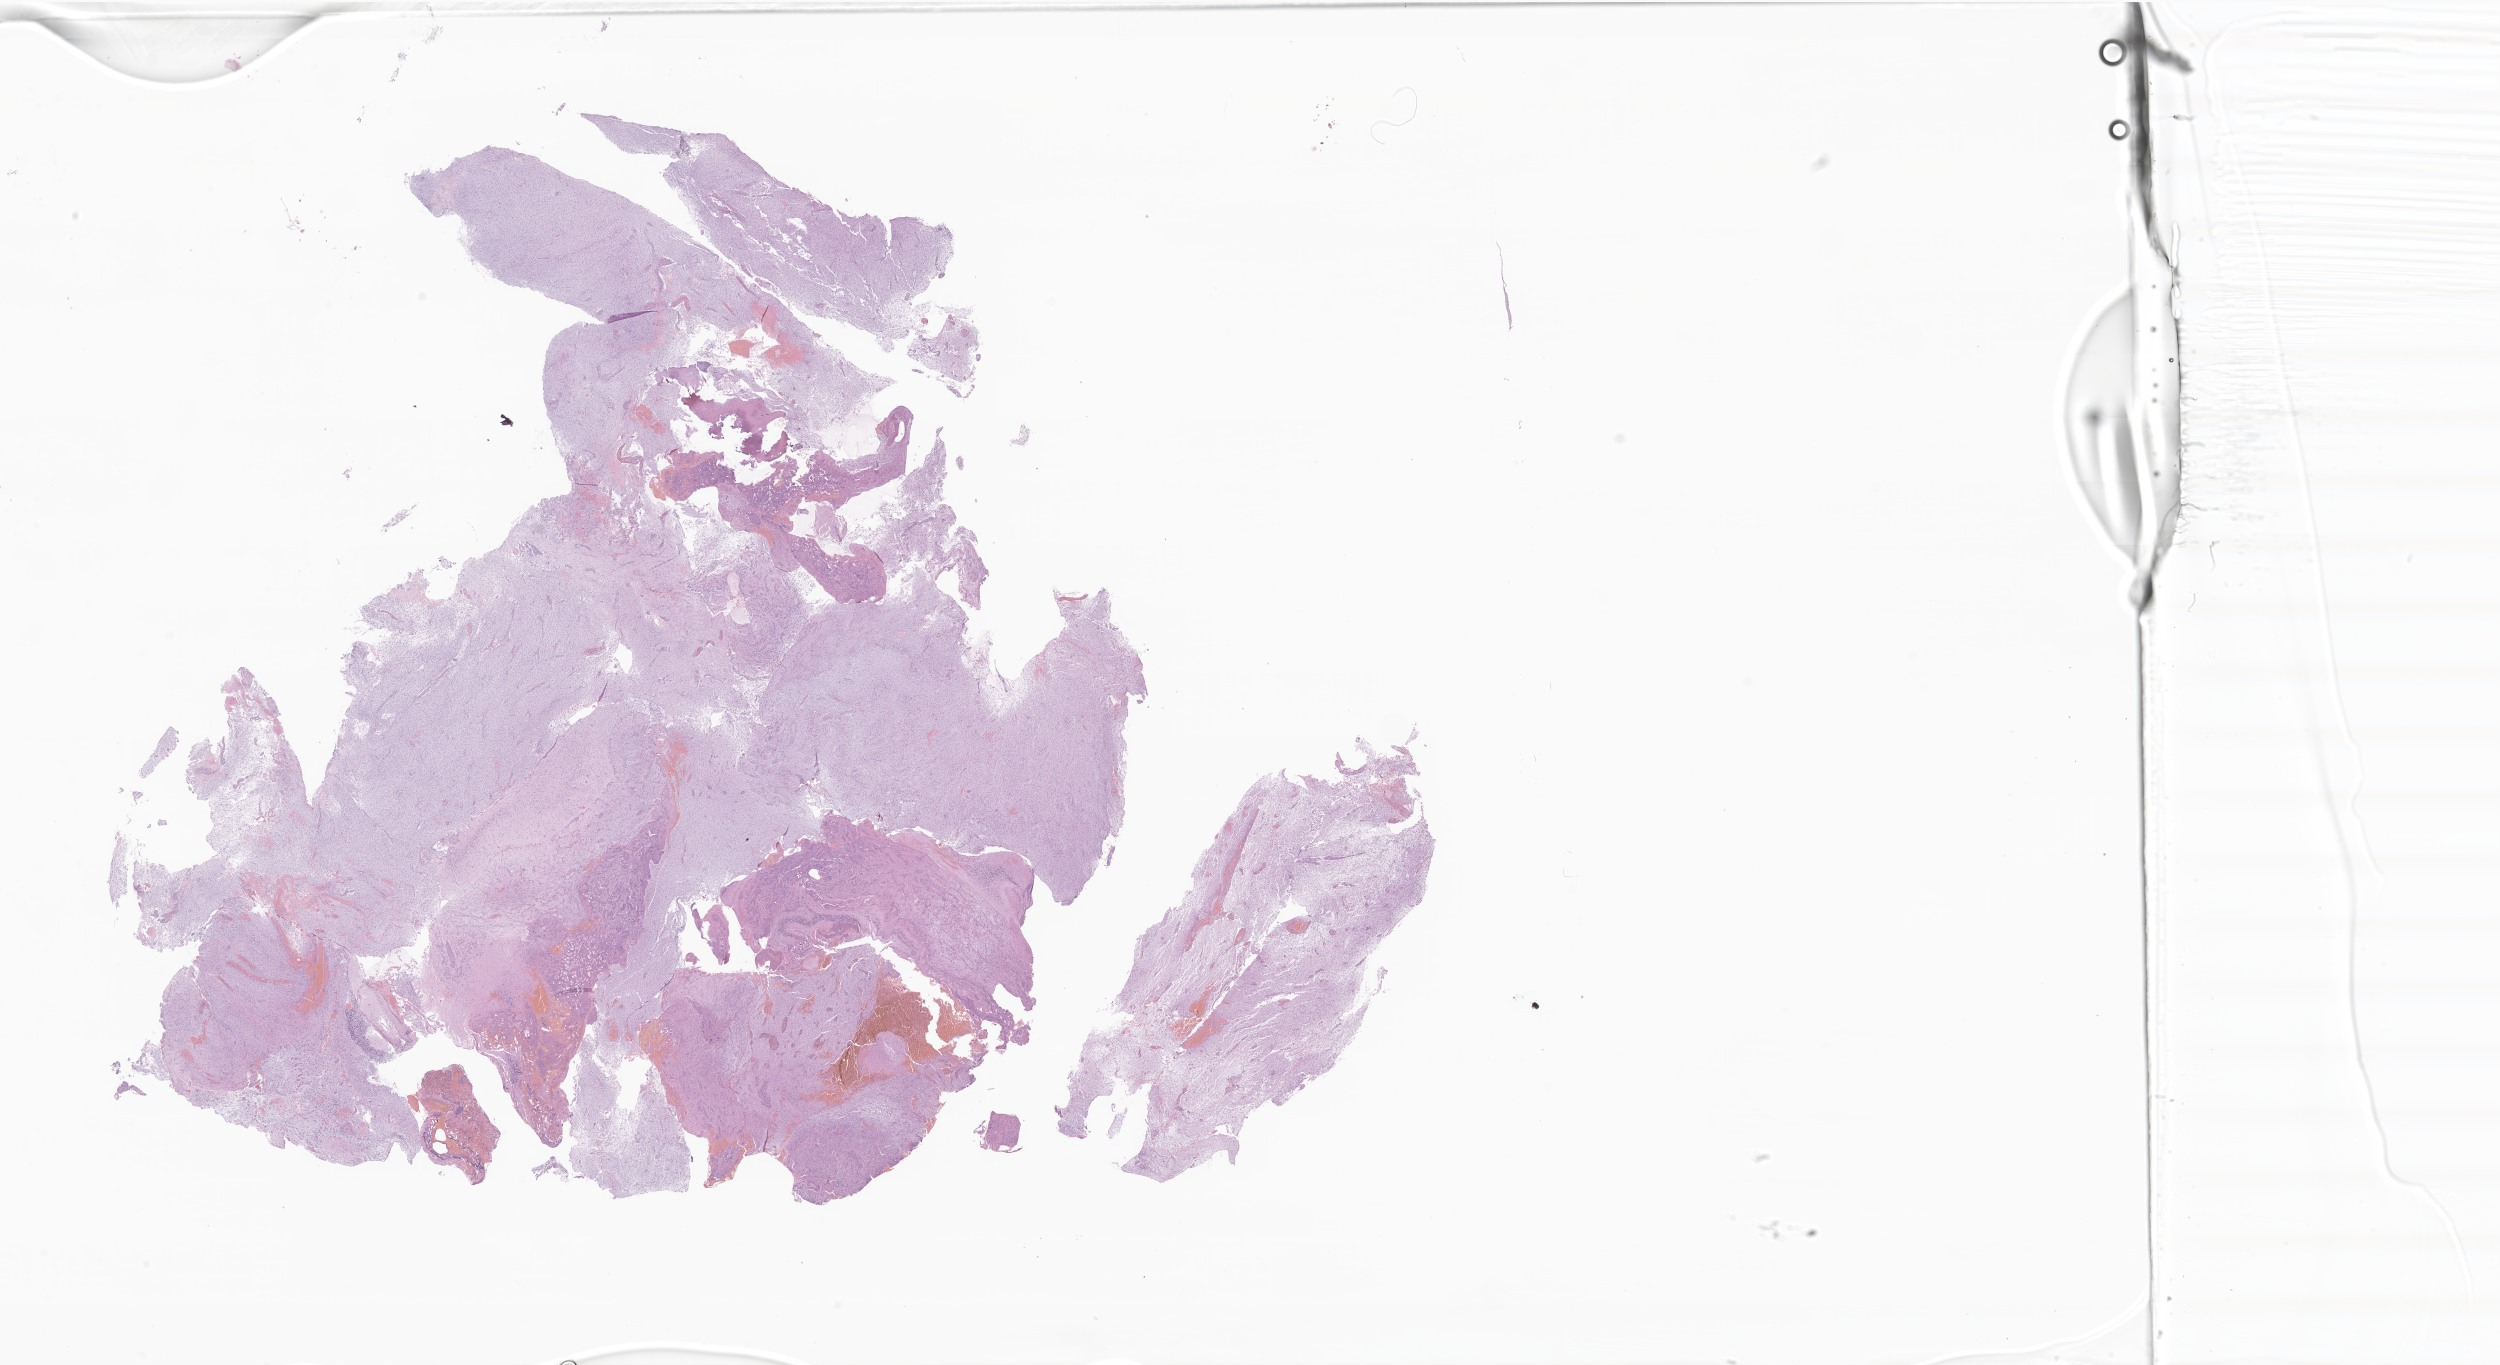
H&E whole-slide image of tumor tissue from the brain, whole scanned area (about 42.2 x 23.0 mm) shown as a low-resolution overview; formalin-fixed, paraffin-embedded (FFPE) tissue. Male patient, age 80 months (6 years 8 months).
Recorded diagnosis: Pilocytic astrocytoma.